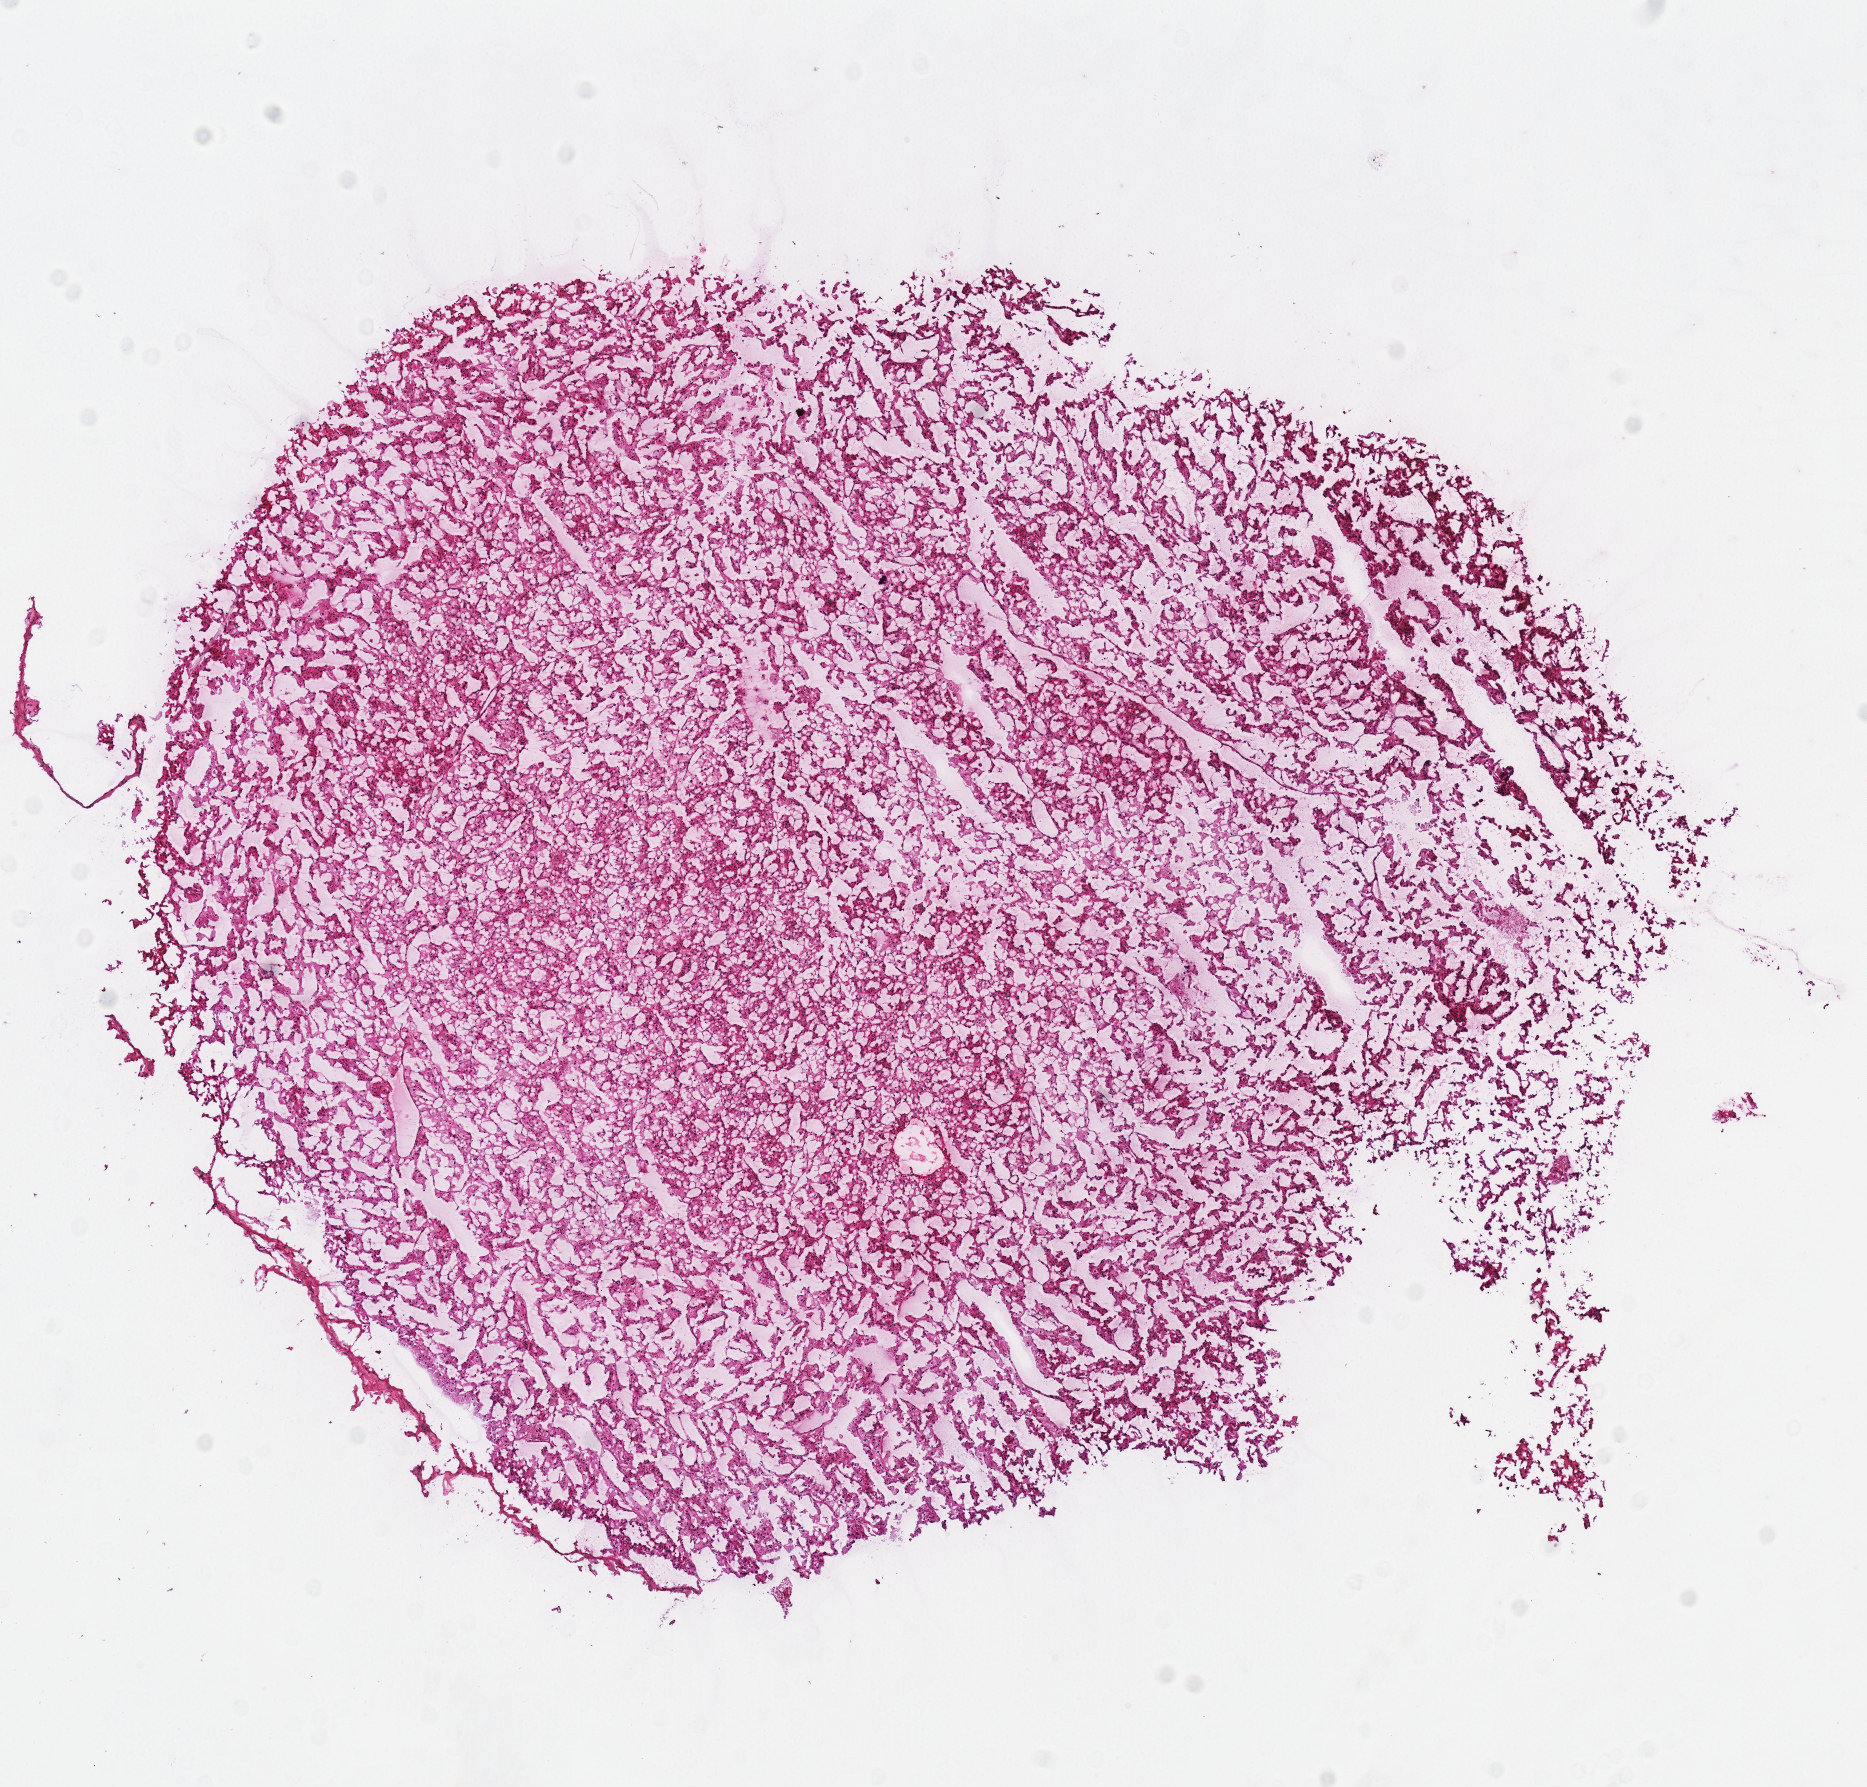
Hematoxylin and eosin (H&E) stained whole-slide image — a low-resolution overview of the entire scanned area, about 7.3 x 7.0 mm. Frozen section from the top of the tissue portion. Sample: primary tumour, kidney. Patient: female, age at initial diagnosis 17 years. Composition of this section per pathologist review: tumour cells 90%, tumour nuclei 90%, normal cells 0%, stromal cells 10%, necrosis 0%.
TNM: T1 N0 M0. Diagnosis: Renal cell carcinoma, chromophobe type. AJCC pathologic stage: I.